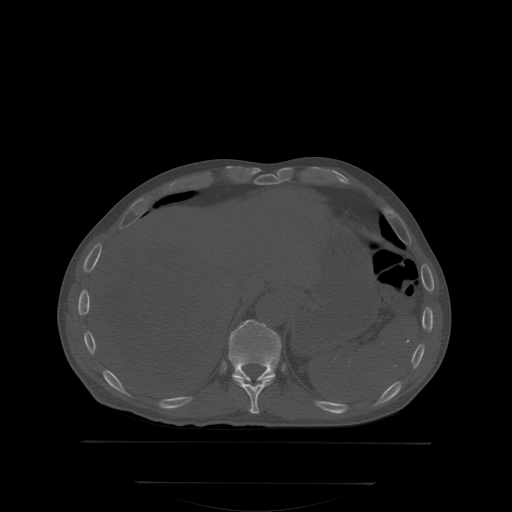
CT including the spine, one axial slice; slice 187 of 350 in the series (ordered by position); bone window (W 1800 / L 400 HU); 2.5 mm slice thickness; 512 × 512 image matrix. Male patient, age 58 years. From the clinical record (not read from this slice): primary cancer: prostate; vertebrae with lytic lesions (as recorded): L1.
Annotated regions visible in this slice (semi-automatically segmented with operator editing):
- T10 vertebra: bounding box (x1, y1, x2, y2) in pixels: (234, 379, 275, 413)
- T11 vertebra: (229, 320, 280, 381)